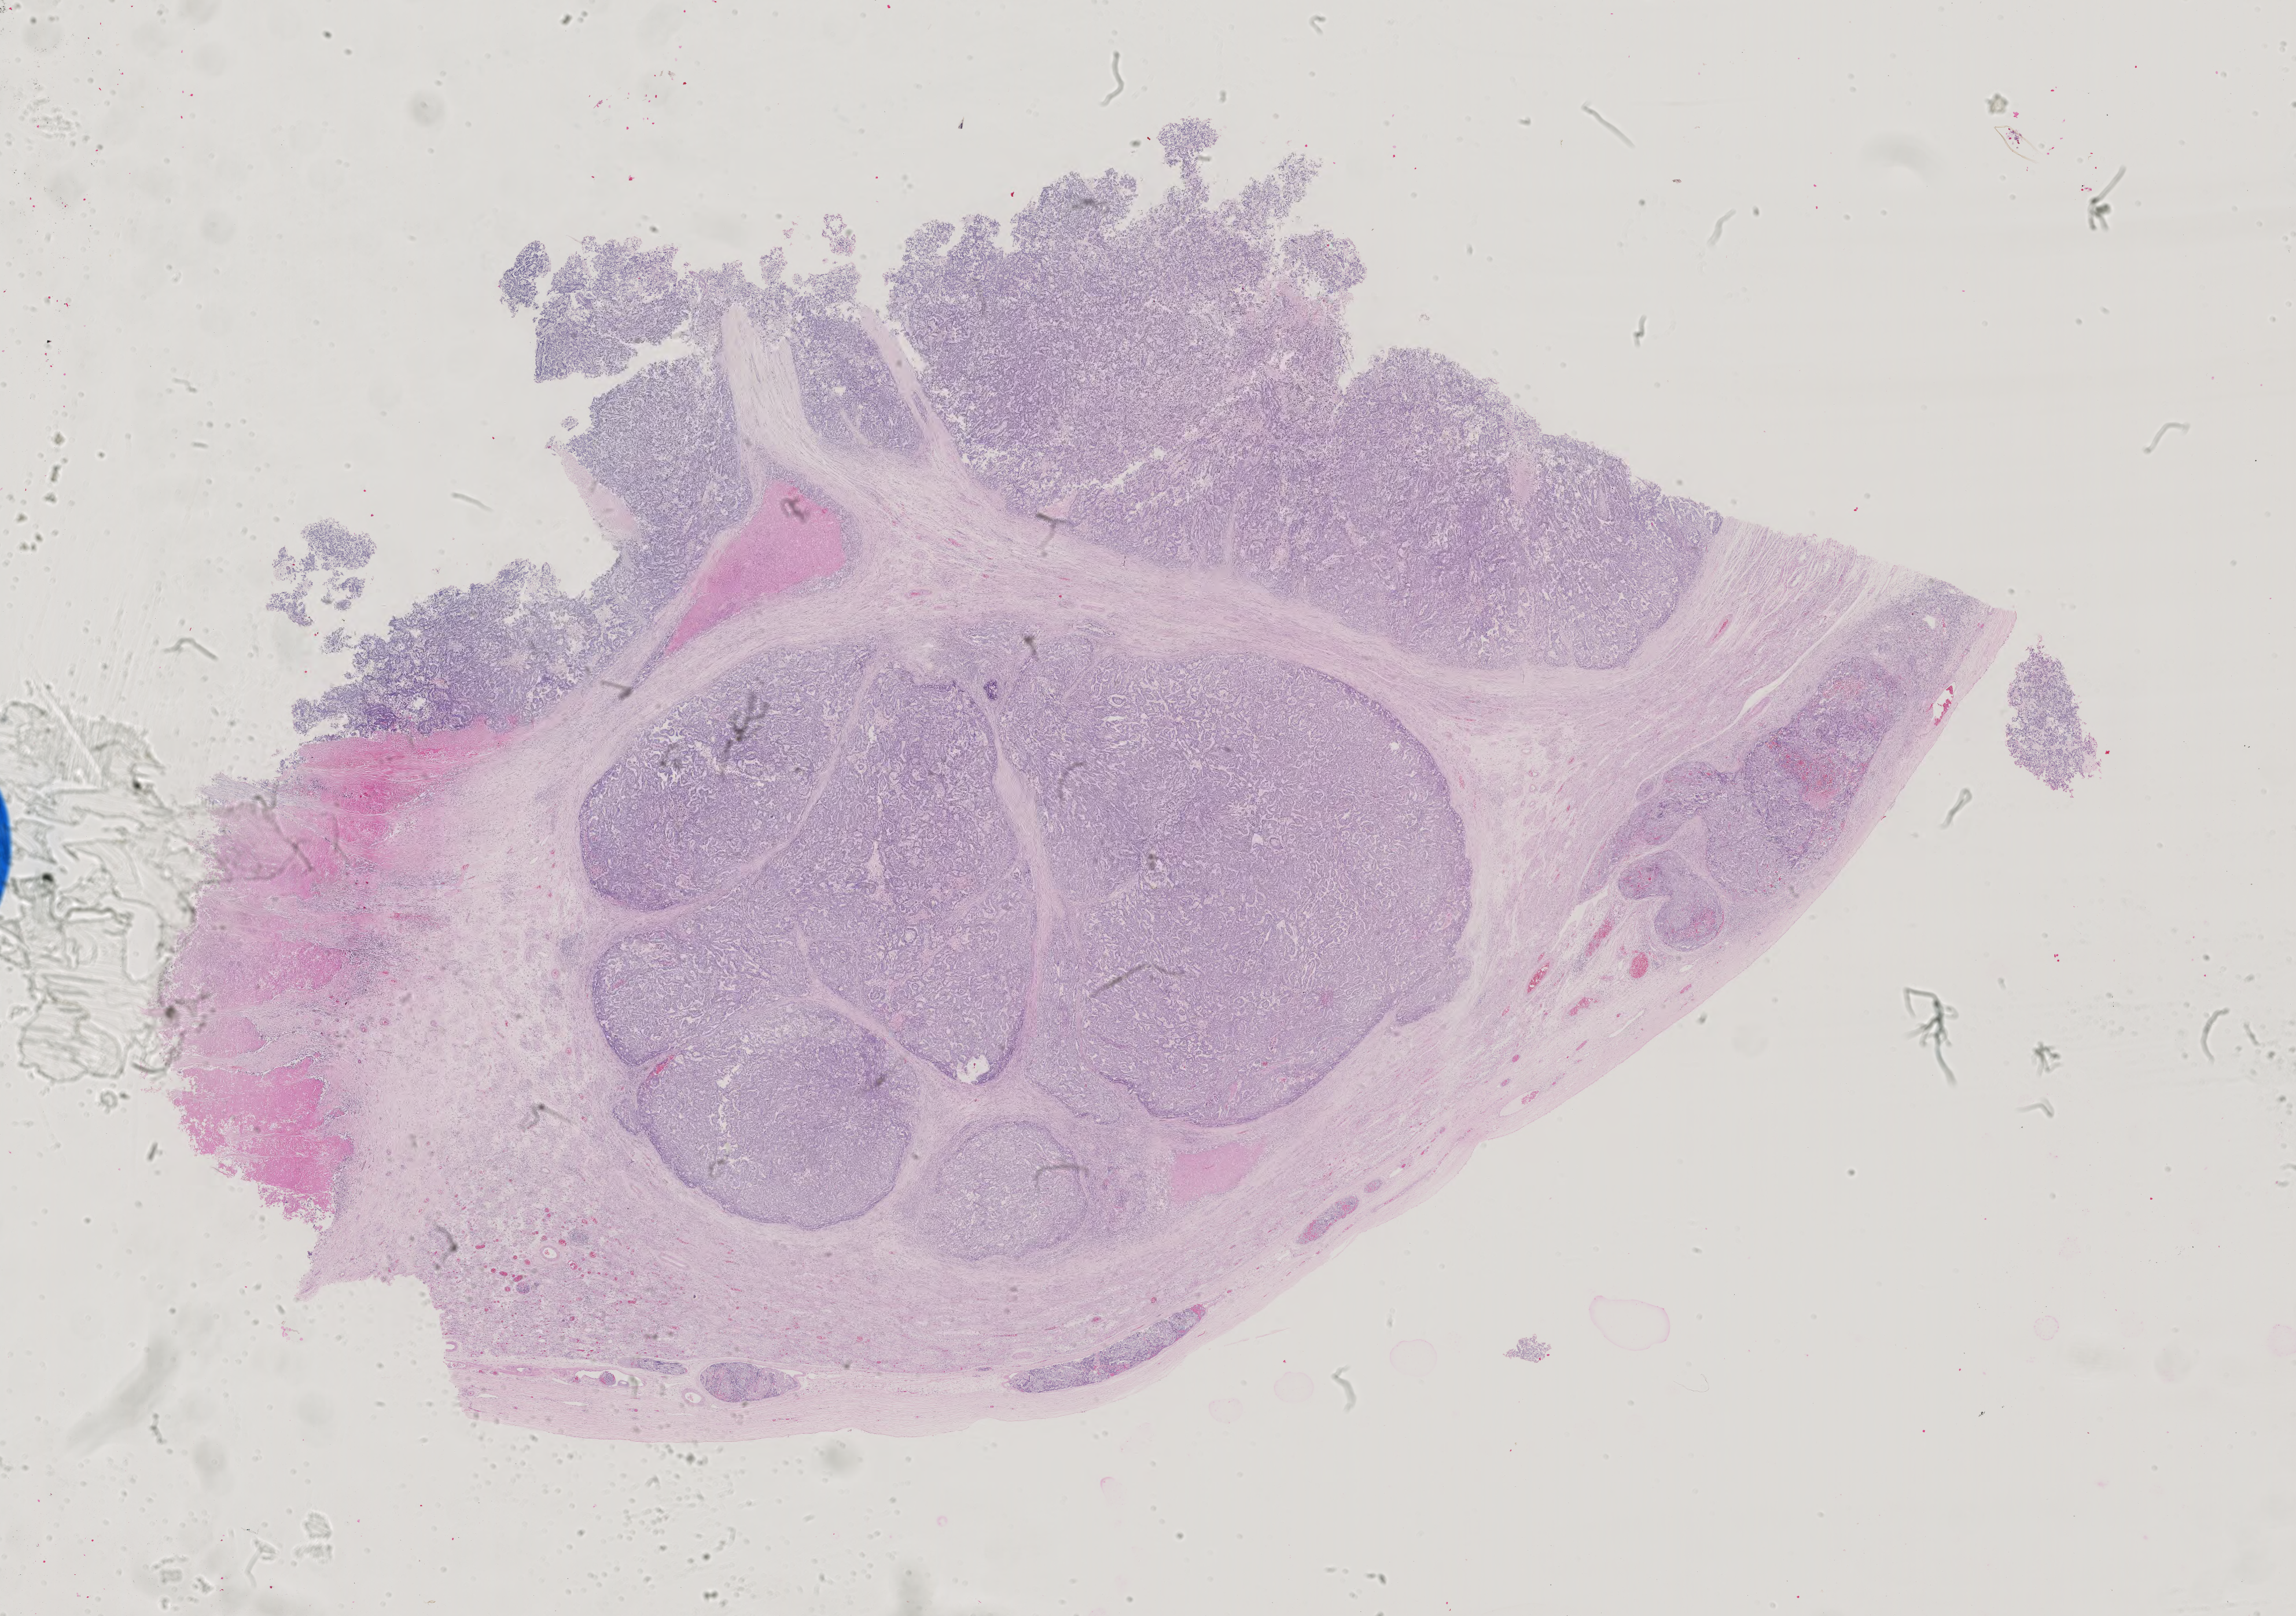
Digitized H&E tissue section (whole slide), shown as a low-resolution overview of the whole scanned area (about 28.9 x 20.3 mm, from a 40x scan). Male patient.
Specimen: FFPE section; testis, primary tumour sample.